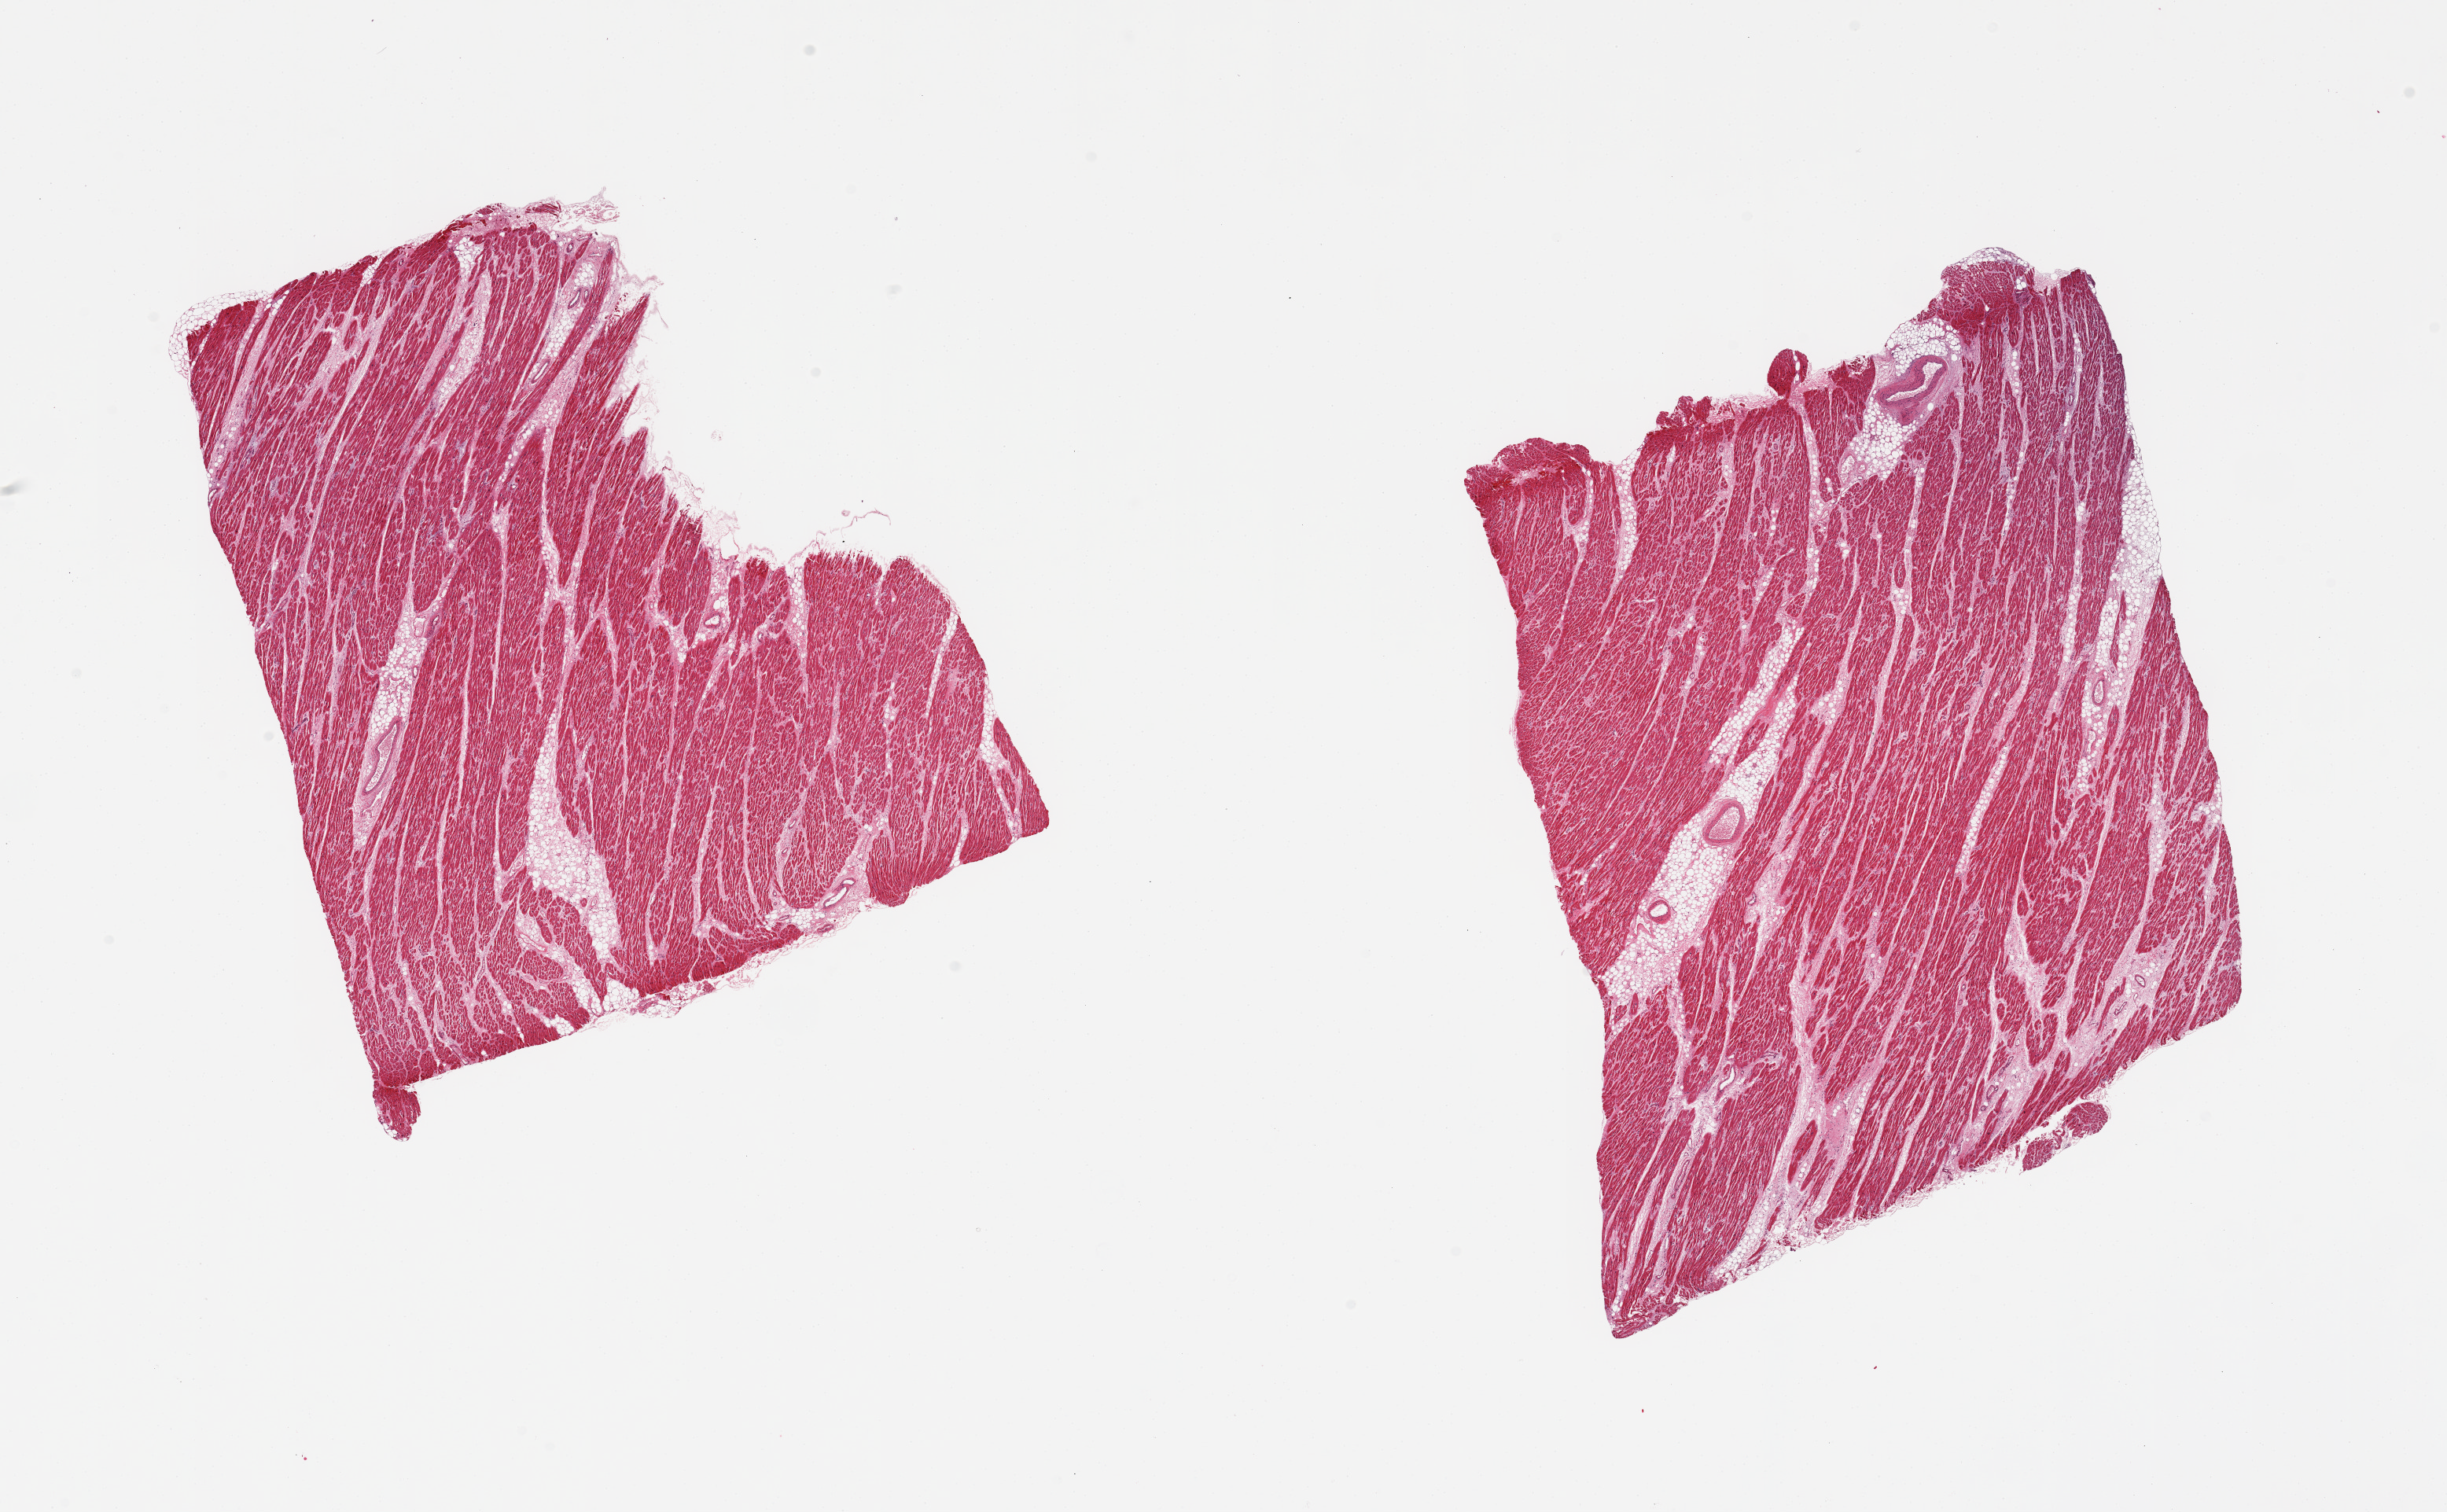
Digitized haematoxylin and eosin-stained section, brightfield, low-resolution overview of the scanned area, about 24.6 x 15.2 mm (slide scanned at 20x), PAXgene-fixed paraffin-embedded (PFPE) section, section of heart (target tissue), tissue donor sample. Donor sex: male.
• reviewer comment on this tissue sample: 2 pieces; 10-15% internal fat, interstitial fibrosis